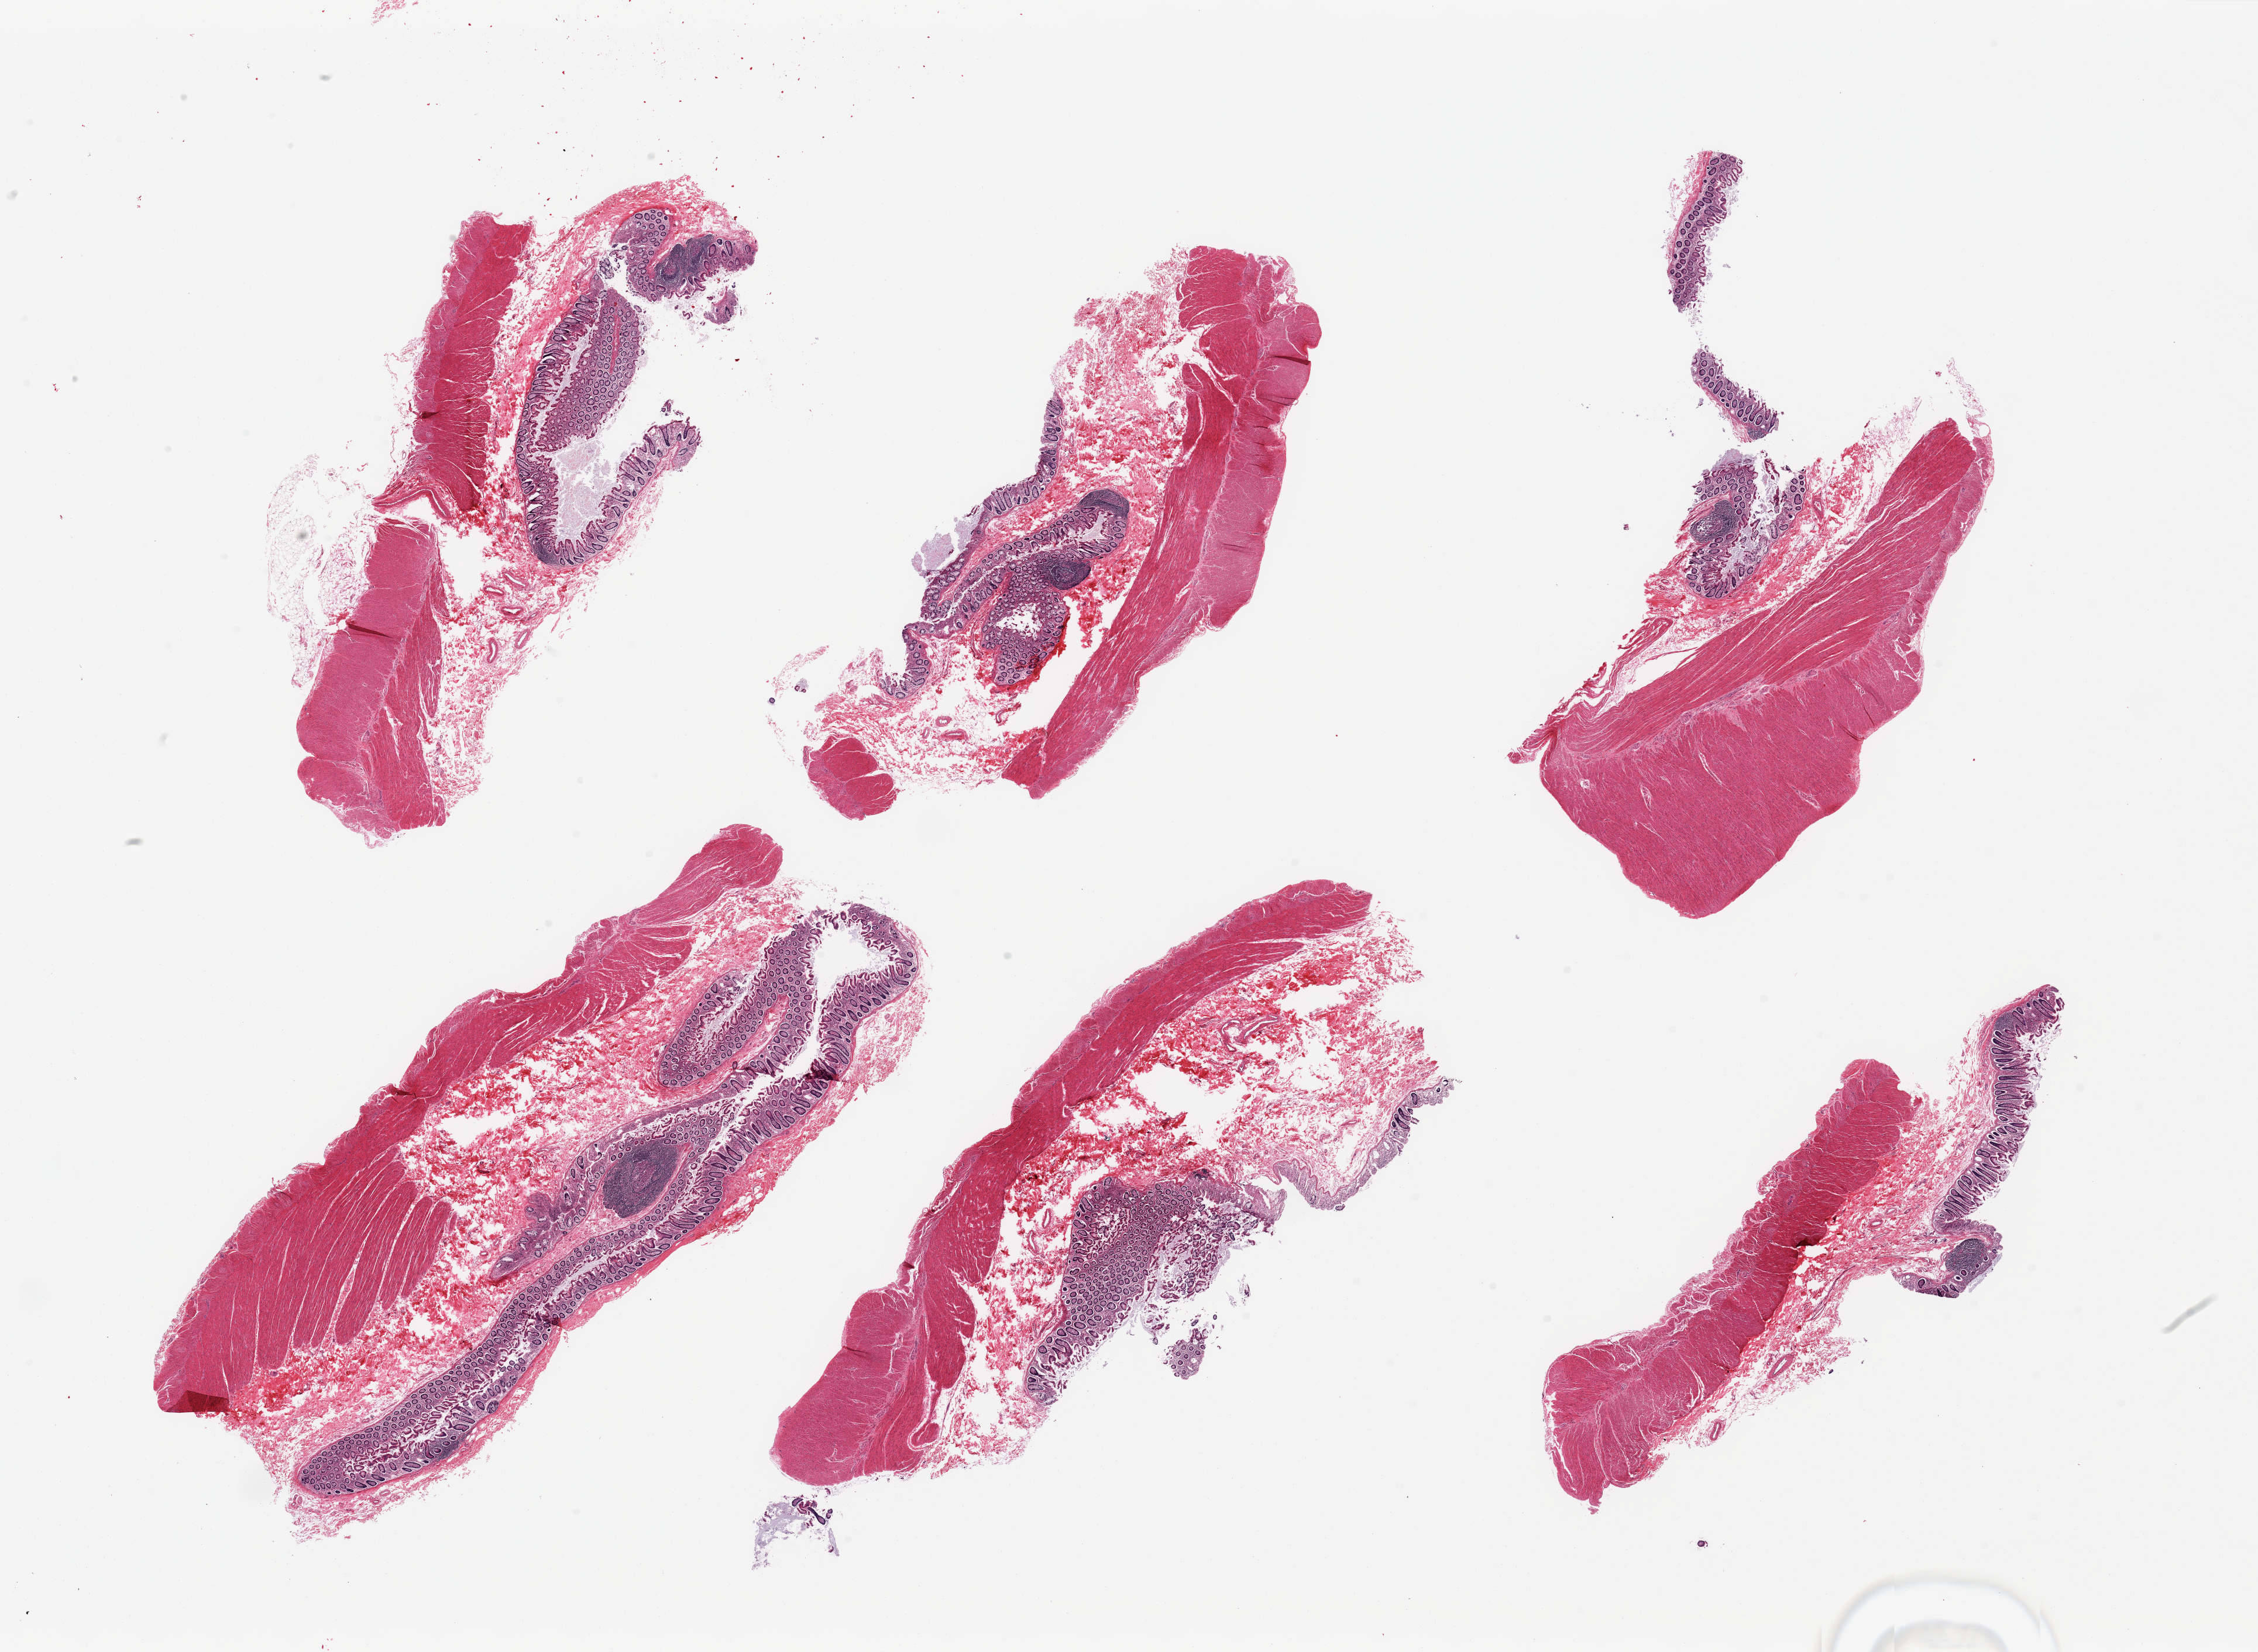
Whole-slide image, hematoxylin and eosin (H&E) stain, whole scanned area (about 30.5 x 22.3 mm, acquisition: 20x scan) shown as a low-resolution overview. PAXgene-fixed paraffin-embedded (PFPE) section. Section of transverse colon (target tissue). Donor tissue sample. Donor: male.
- reviewer comment on this tissue sample: 6 pieces; all full thickness